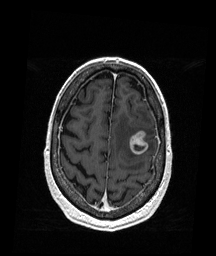
Brain MRI from a brain-tumour surgery series, one axial slice; slice 48 of 176 in the series (ordered by position); T1-weighted post-contrast; 1 mm slice thickness; 216 × 256 image matrix. Case-level facts recorded for this patient, not image findings: histopathology: Metastatic Melanoma.
Structures marked on this image (outlined manually by an expert reader):
- tumour: bounding box (x1, y1, x2, y2) in pixels: (129, 130, 149, 154)